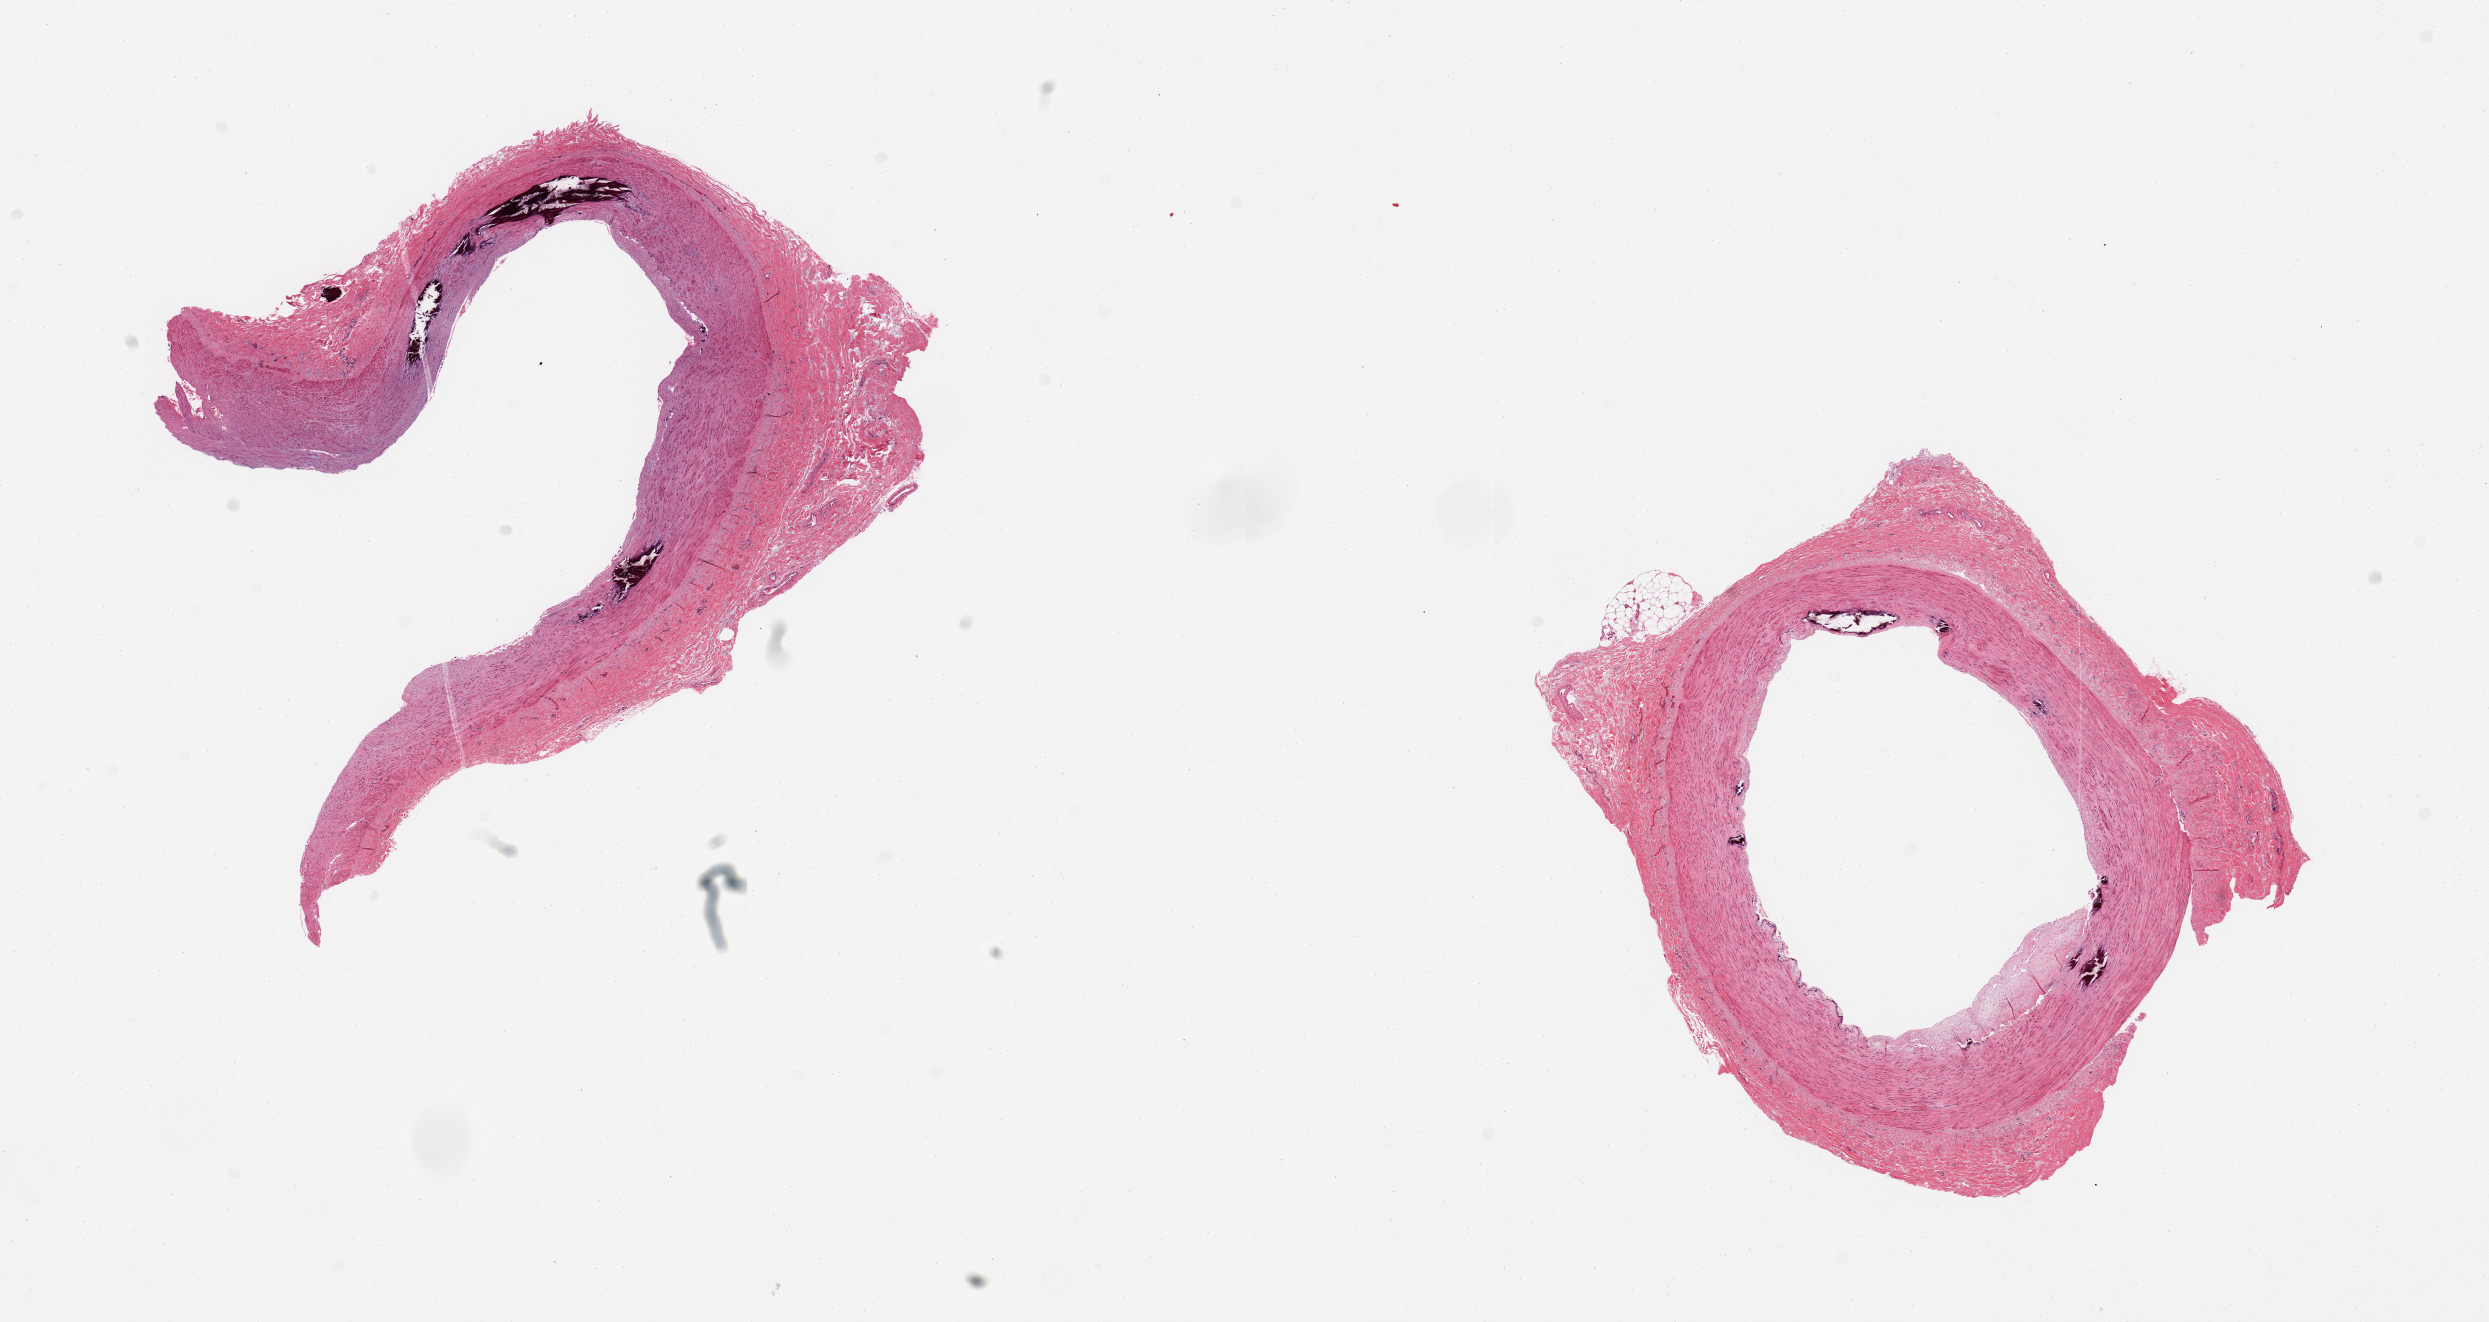
Whole-slide image, hematoxylin and eosin (H&E) stain, low-resolution overview of the scanned area, about 19.7 x 10.5 mm (from a 20x scan), PAXgene-fixed, paraffin-embedded tissue, target tissue: tibial artery, donor tissue sample. Donor: male.
Pathologist's review note for this sample: 2 pieces, foci of Monckebergs medial sclerosis, adherent fibrous tissue up to 0.7mm.